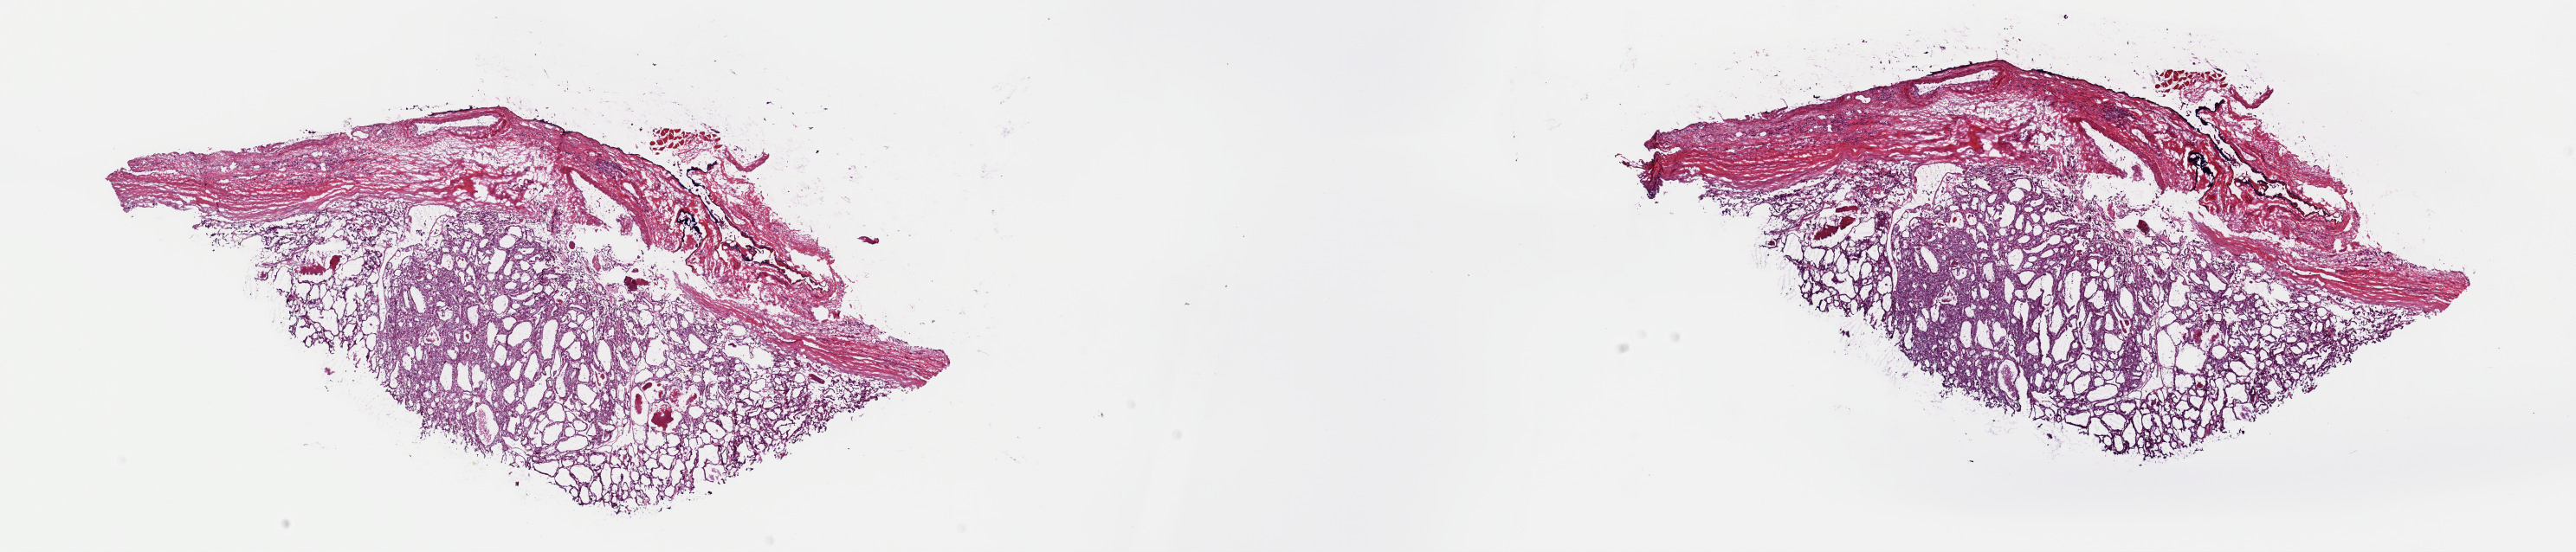
H&E whole-slide image, whole scanned area (about 23.5 x 5.0 mm) shown as a low-resolution overview; frozen section from the top of the tissue portion; sample: primary tumour, thyroid. Female, age 68 years at initial diagnosis. Slide review estimates, as recorded: tumour cells 70%, tumour nuclei 97%, normal cells 3%, stromal cells 27%, necrosis 0%. Infiltration values recorded for this section: lymphocyte infiltration 2%, monocyte infiltration 0%, neutrophil infiltration 0%.
* AJCC pathologic stage: II (7th edition)
* pathologic diagnosis: Papillary carcinoma, follicular variant (thyroid gland)